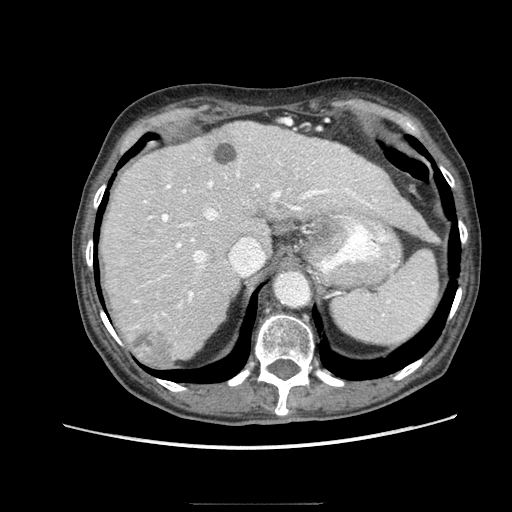
Contrast-enhanced abdominal CT (liver protocol), one axial slice. Slice 62 of 83 in the series (ordered by position). Reconstruction kernel STANDARD. 140 kVp. Soft-tissue window (W 400 / L 40 HU). 512 × 512 image matrix, field of view 360 × 360 mm. From the clinical record (not read from this slice): diagnosis: hepatocellular carcinoma (patient treated with transarterial chemoembolisation; whether this scan precedes or follows treatment is not stated here); TNM stage (as recorded): Stage-I; Child-Pugh class: A.
Structures marked on this image (semi-automatic segmentation, software-assisted and operator-edited):
- abdominal aorta: box from (x=275, y=272) to (x=311, y=306) px
- liver parenchyma outside the tumour (the mass and vessels are separate outlines, so this box may not span the whole liver): (x=100, y=122)–(x=424, y=360)
- mass: (x=131, y=331)–(x=179, y=367)
- liver vessels: (x=134, y=138)–(x=380, y=328)